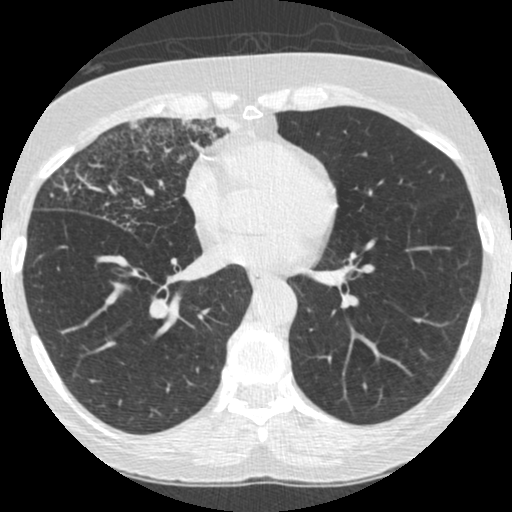
Low-dose screening chest CT, one axial slice; slice 119 of 253 in the series (ordered by position); reconstruction kernel STANDARD; 120 kVp; lung window (W 1500 / L -600 HU); 1.25 mm slice thickness; 512 × 512 image matrix.
Annotated regions visible in this slice (manually delineated by an expert):
- lesion 4 (tumor, upper lobe of right lung): bounding box <182,115,237,151> (left, top, right, bottom; pixels)